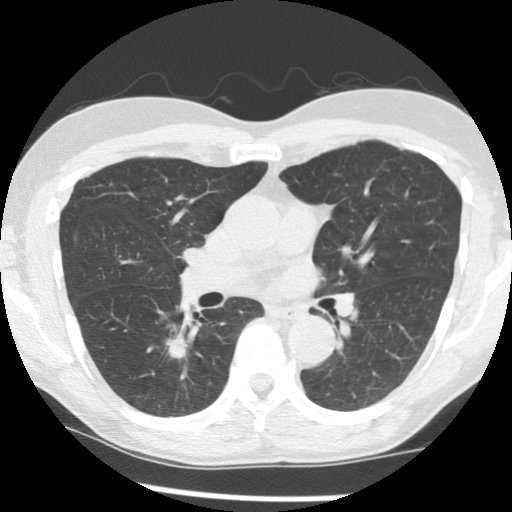
Chest CT (low-dose screening protocol), one axial image, third screening round (two years after baseline), lung window (W 1500 / L -600 HU), 2.5 mm slice thickness, standard (soft-tissue) reconstruction kernel (STANDARD), slice 78 of 145 in the series. Male, age 65 years at enrolment.
- Expert reader's lesion annotation, box from (x=146, y=321) to (x=205, y=376) px.
- The screening reader recorded 2 non-calcified nodules or masses ≥4 mm on this exam; which of them this box marks is not recorded.
- Official screen result: positive, other.